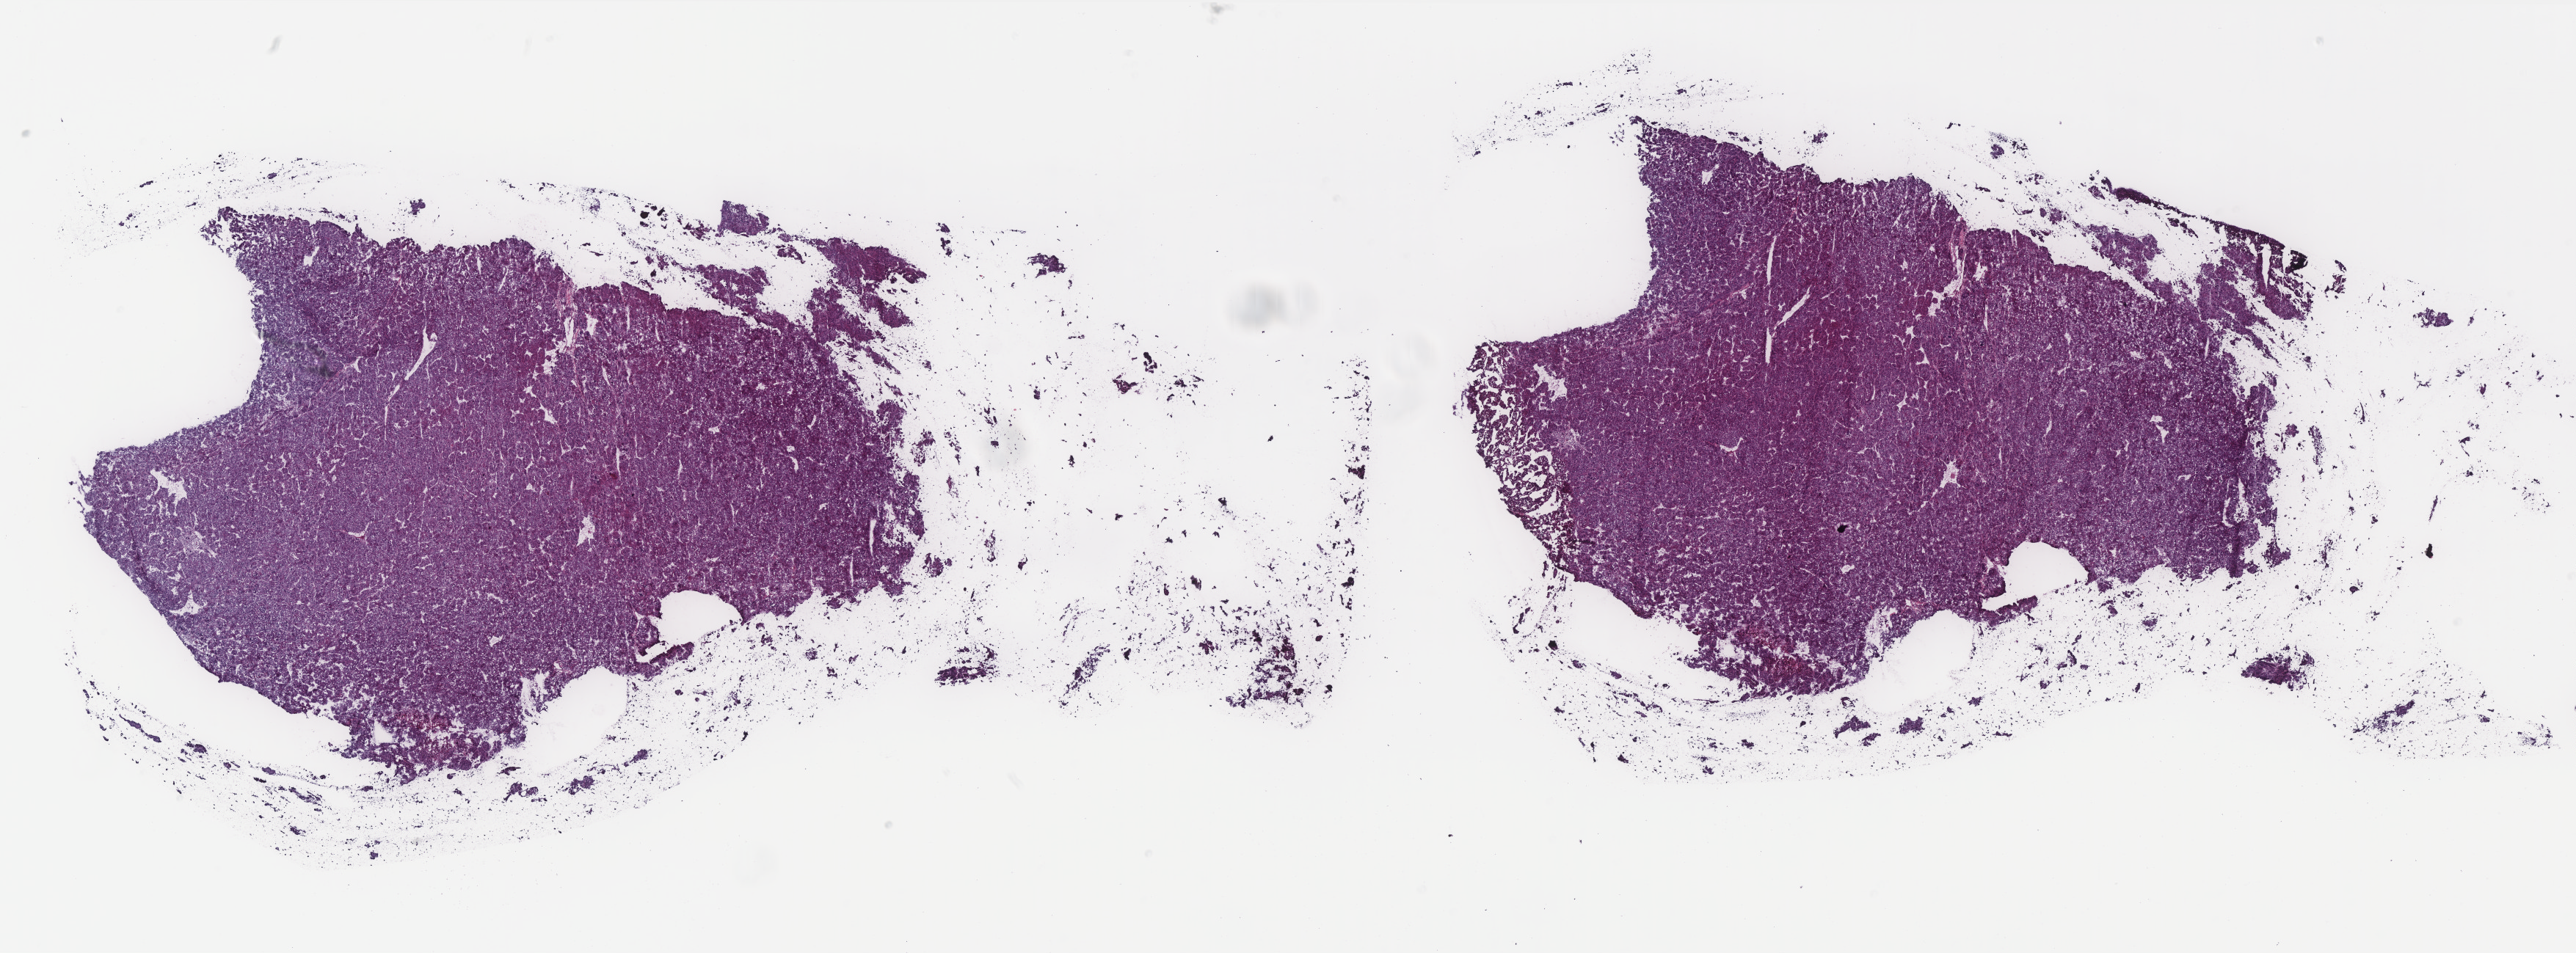
Whole-slide histology image, H&E, a low-resolution overview of the entire scanned area, about 28.1 x 10.4 mm (acquisition: 40x scan); frozen section from the top of the tissue portion; liver, primary tumour sample. Male patient; age at initial diagnosis 23 years. Histologic grade: G3 (poorly differentiated). Slide review estimates, as recorded: tumour cells 90%, tumour nuclei 90%, normal cells 0%, stromal cells 10%, necrosis 0%. Inflammatory infiltration, as recorded: lymphocyte infiltration 3%, monocyte infiltration 0%, neutrophil infiltration 0%.
AJCC pathologic stage: II. Histologic diagnosis: Hepatocellular carcinoma, NOS.